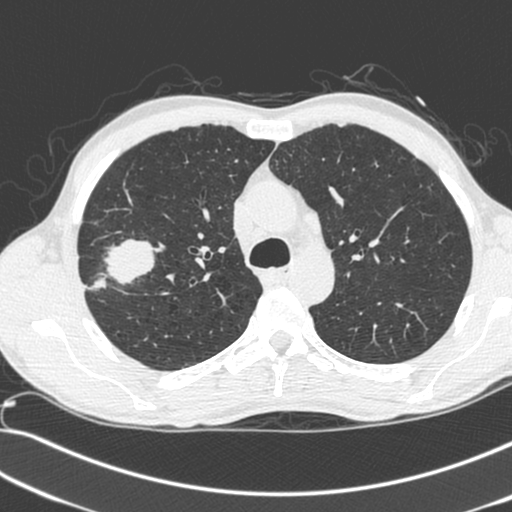
Low-dose screening chest CT, axial slice. Baseline screening round. Lung window (W 1500 / L -600 HU). 1.3 mm slice thickness. Standard (soft-tissue) reconstruction kernel (C). Male participant, aged 55 years at enrolment.
Expert-annotated lung lesion, box from (x=72, y=235) to (x=151, y=307) px. Screening reader's record for this exam (one nodule recorded; not confirmed to be the boxed lesion): non-calcified nodule or mass ≥4 mm, right upper lobe, 52 × 39 mm, spiculated (stellate) margins, soft tissue attenuation. Official screen result: positive, change unspecified: nodule(s) >= 4 mm or enlarging nodule(s), mass(es), or other non-specific abnormalities suspicious for lung cancer. Participant outcome: lung cancer diagnosed 25 days after this screen — large cell neuroendocrine carcinoma, right upper lobe, poorly differentiated (G3), stage IIB (AJCC 6th edition), 49 mm at pathology.